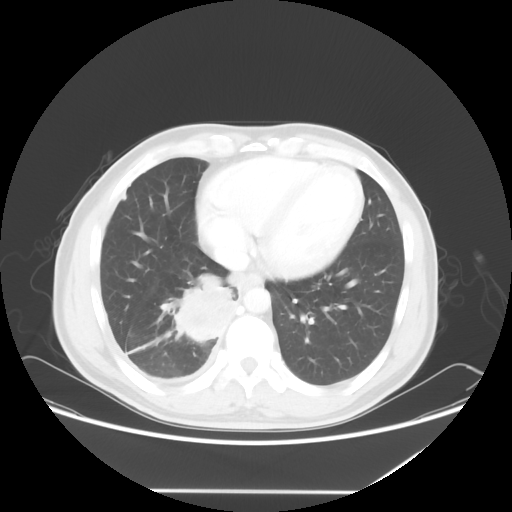
Chest CT, one axial slice. Position 20 of 60 along the scan axis. 120 kVp. Lung window (W 1500 / L -600 HU). 5 mm slice thickness. 512 × 512 image matrix, field of view 419 × 419 mm. Male patient, age 48 years. Case-level facts recorded for this patient, not image findings: clinical TNM (as recorded): T3 N3 M1a.
Structures marked on this image (bounding box drawn by a radiologist):
- lung tumour (recorded histology: squamous cell carcinoma): bounding box <159,265,244,346> (left, top, right, bottom; pixels)